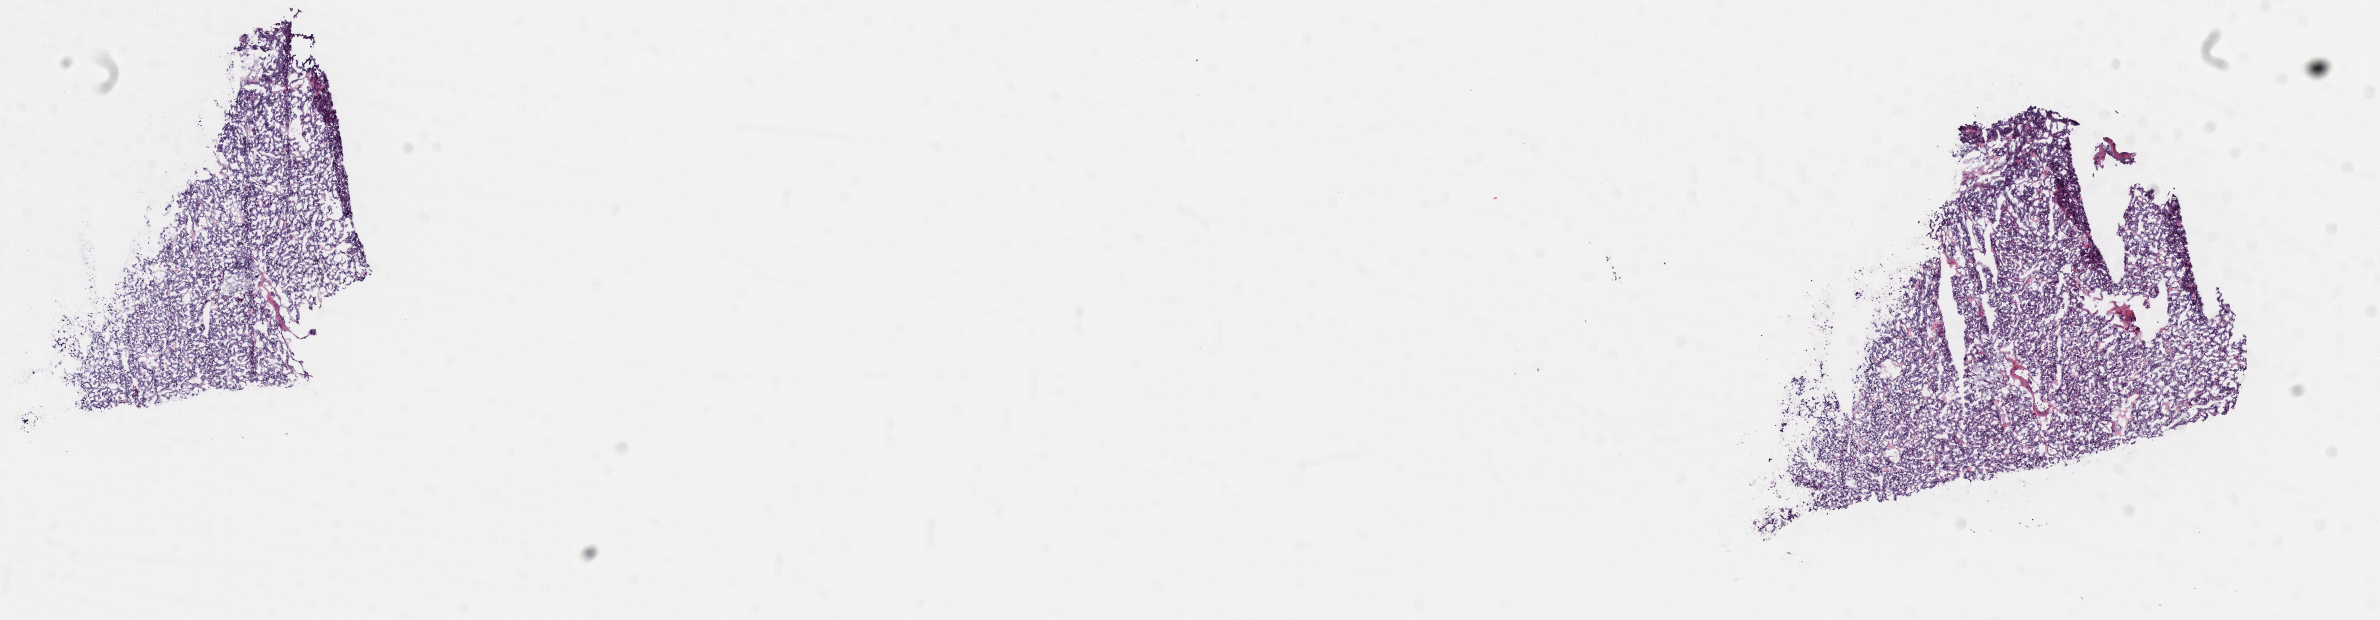
Digitized H&E-stained tissue section (whole slide) — shown as a low-resolution overview of the whole scanned area (about 18.8 x 4.9 mm). Frozen section. Adrenal gland, primary tumour sample. Male, age 47 years at initial diagnosis. Pathologist review of this section (percent, as recorded): tumour cells 85%, tumour nuclei 90%, normal cells 0%, stromal cells 10%, necrosis 5%. Infiltration values recorded for this section: lymphocyte infiltration 0%, monocyte infiltration 0%, neutrophil infiltration 0%.
- lymph nodes positive (case pathology): 0 of 1 examined
- diagnosis: Pheochromocytoma, malignant